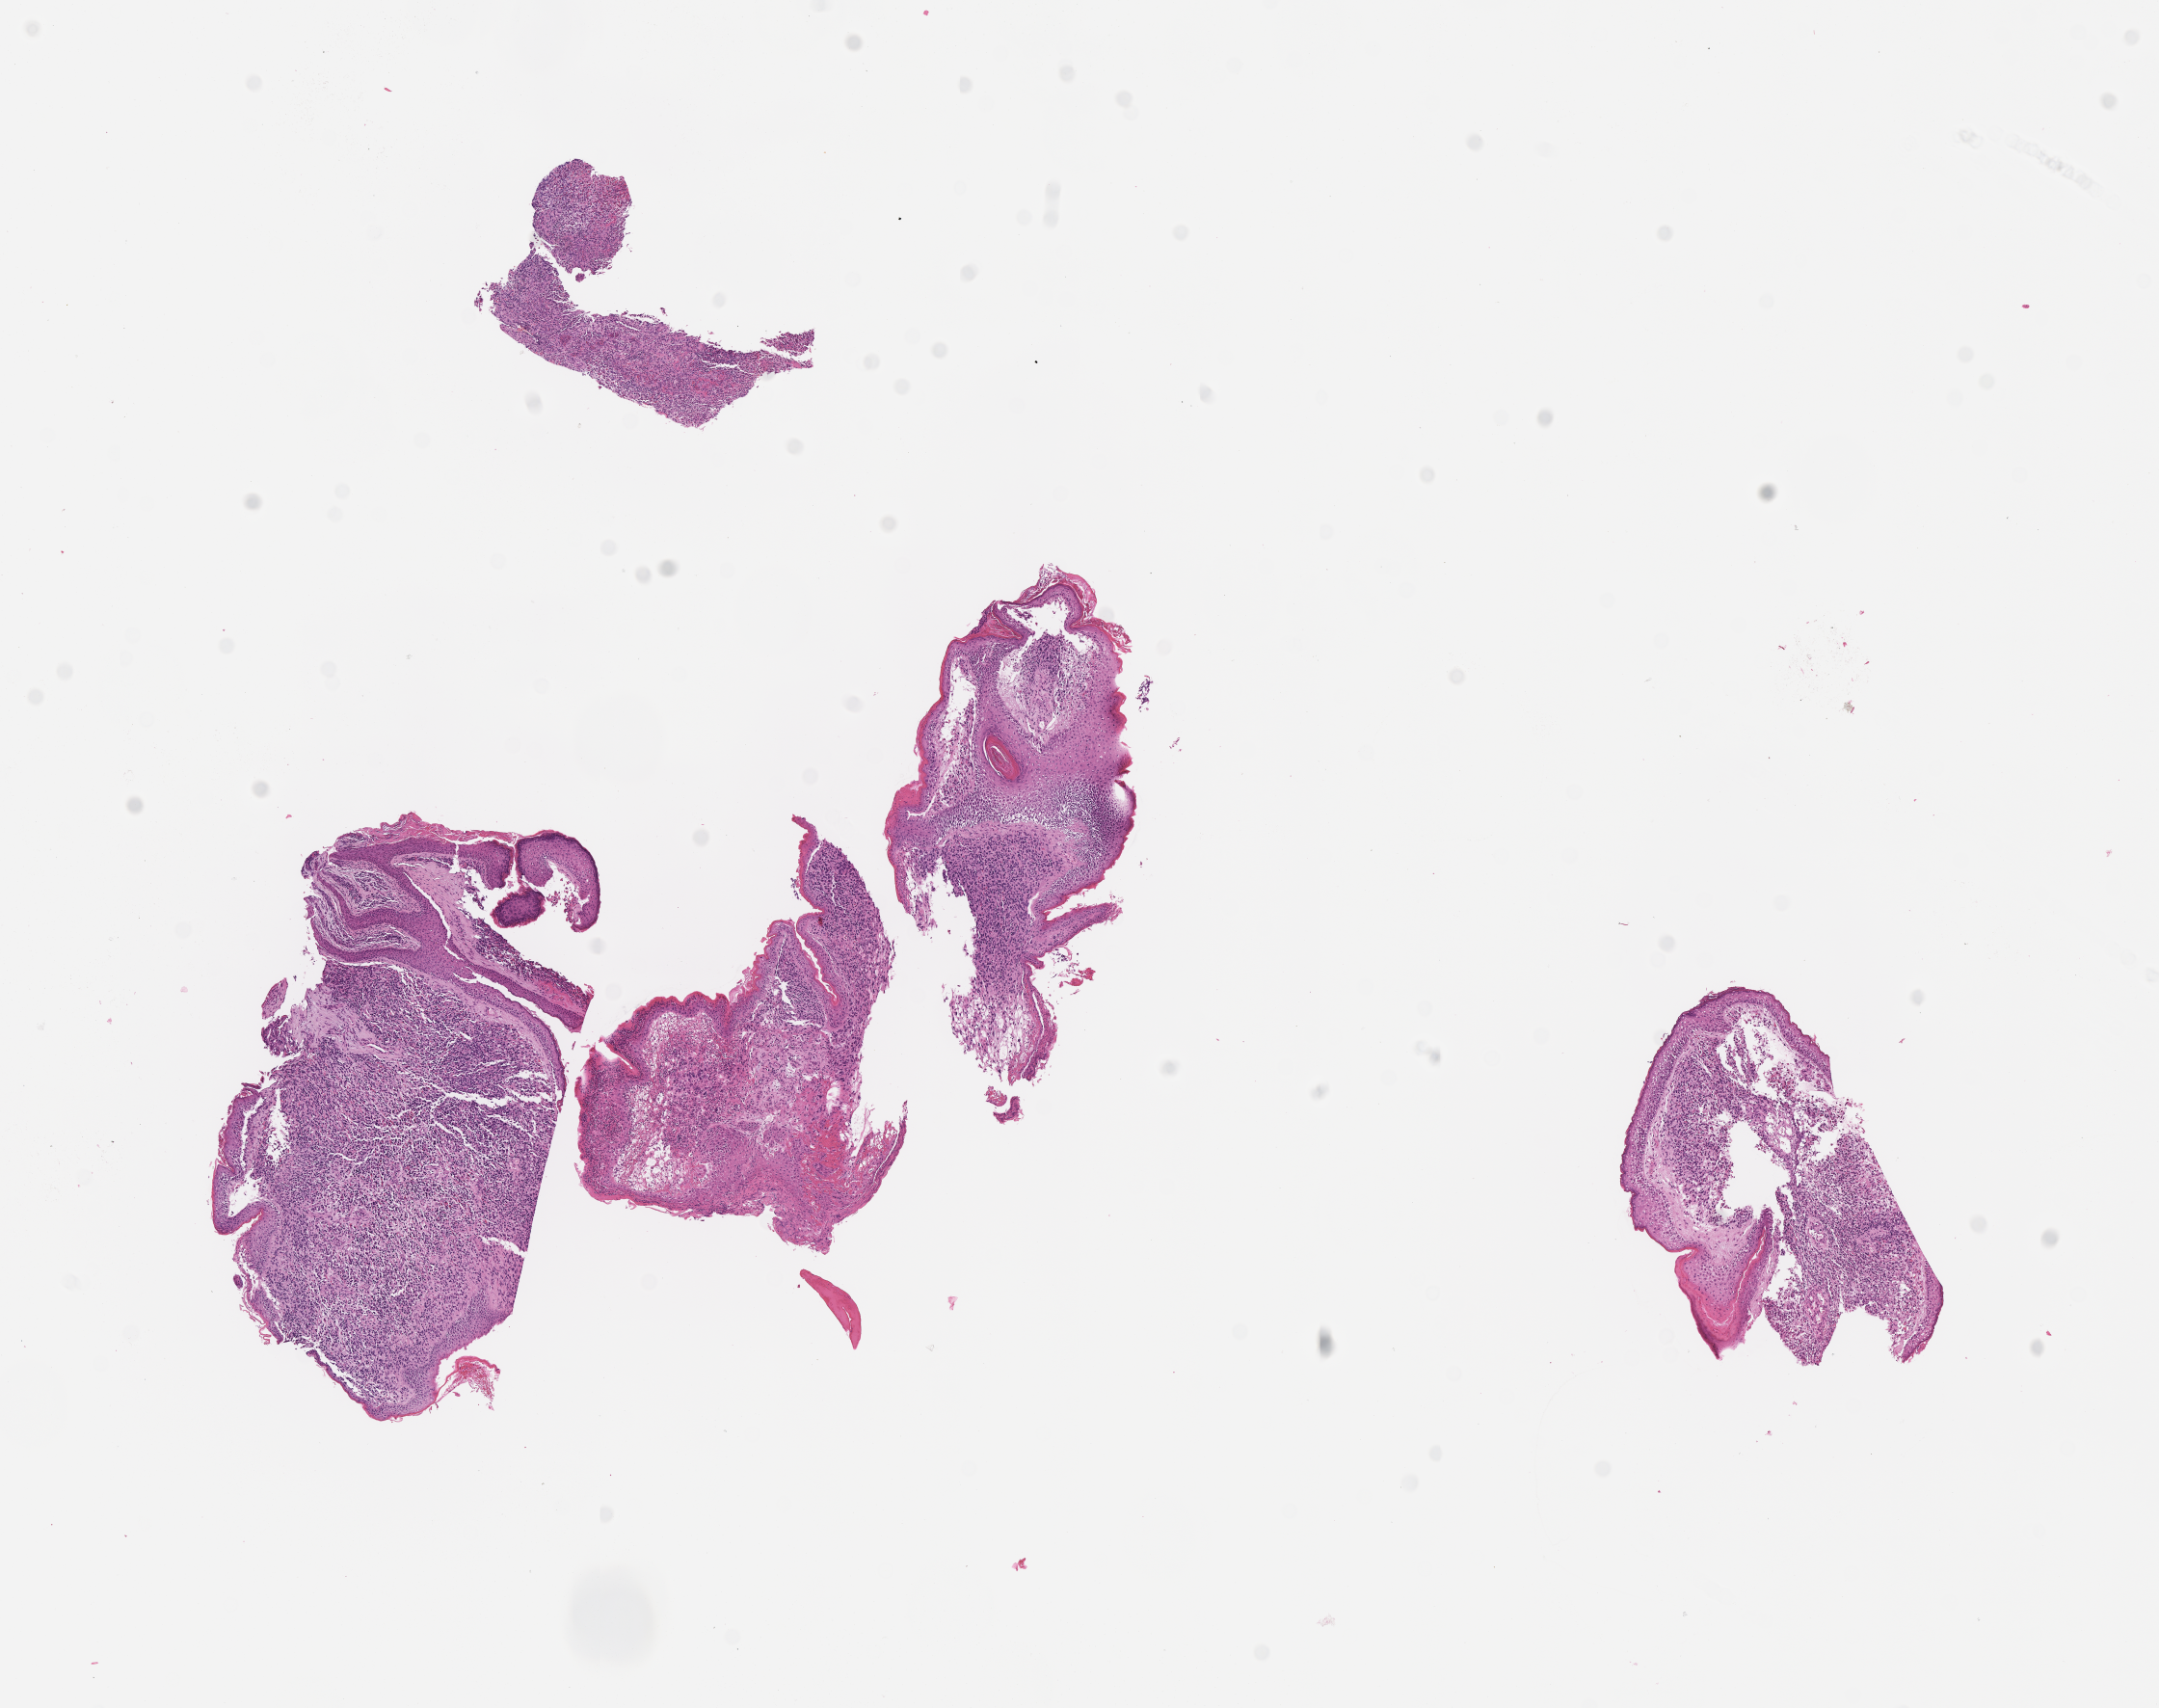
Whole-slide image, H&E stain of tumor tissue, whole scanned area (about 9.1 x 7.2 mm) shown as a low-resolution overview, FFPE section, site: ear, left. Patient: female, age 3.9 years at diagnosis.
Stage (as recorded): 2. Diagnosis: rhabdomyosarcoma; histological classification: embryonal rhabdomyosarcoma. Metastatic status at presentation (as recorded): non-metastatic. Primary site (case record): middle Ear.